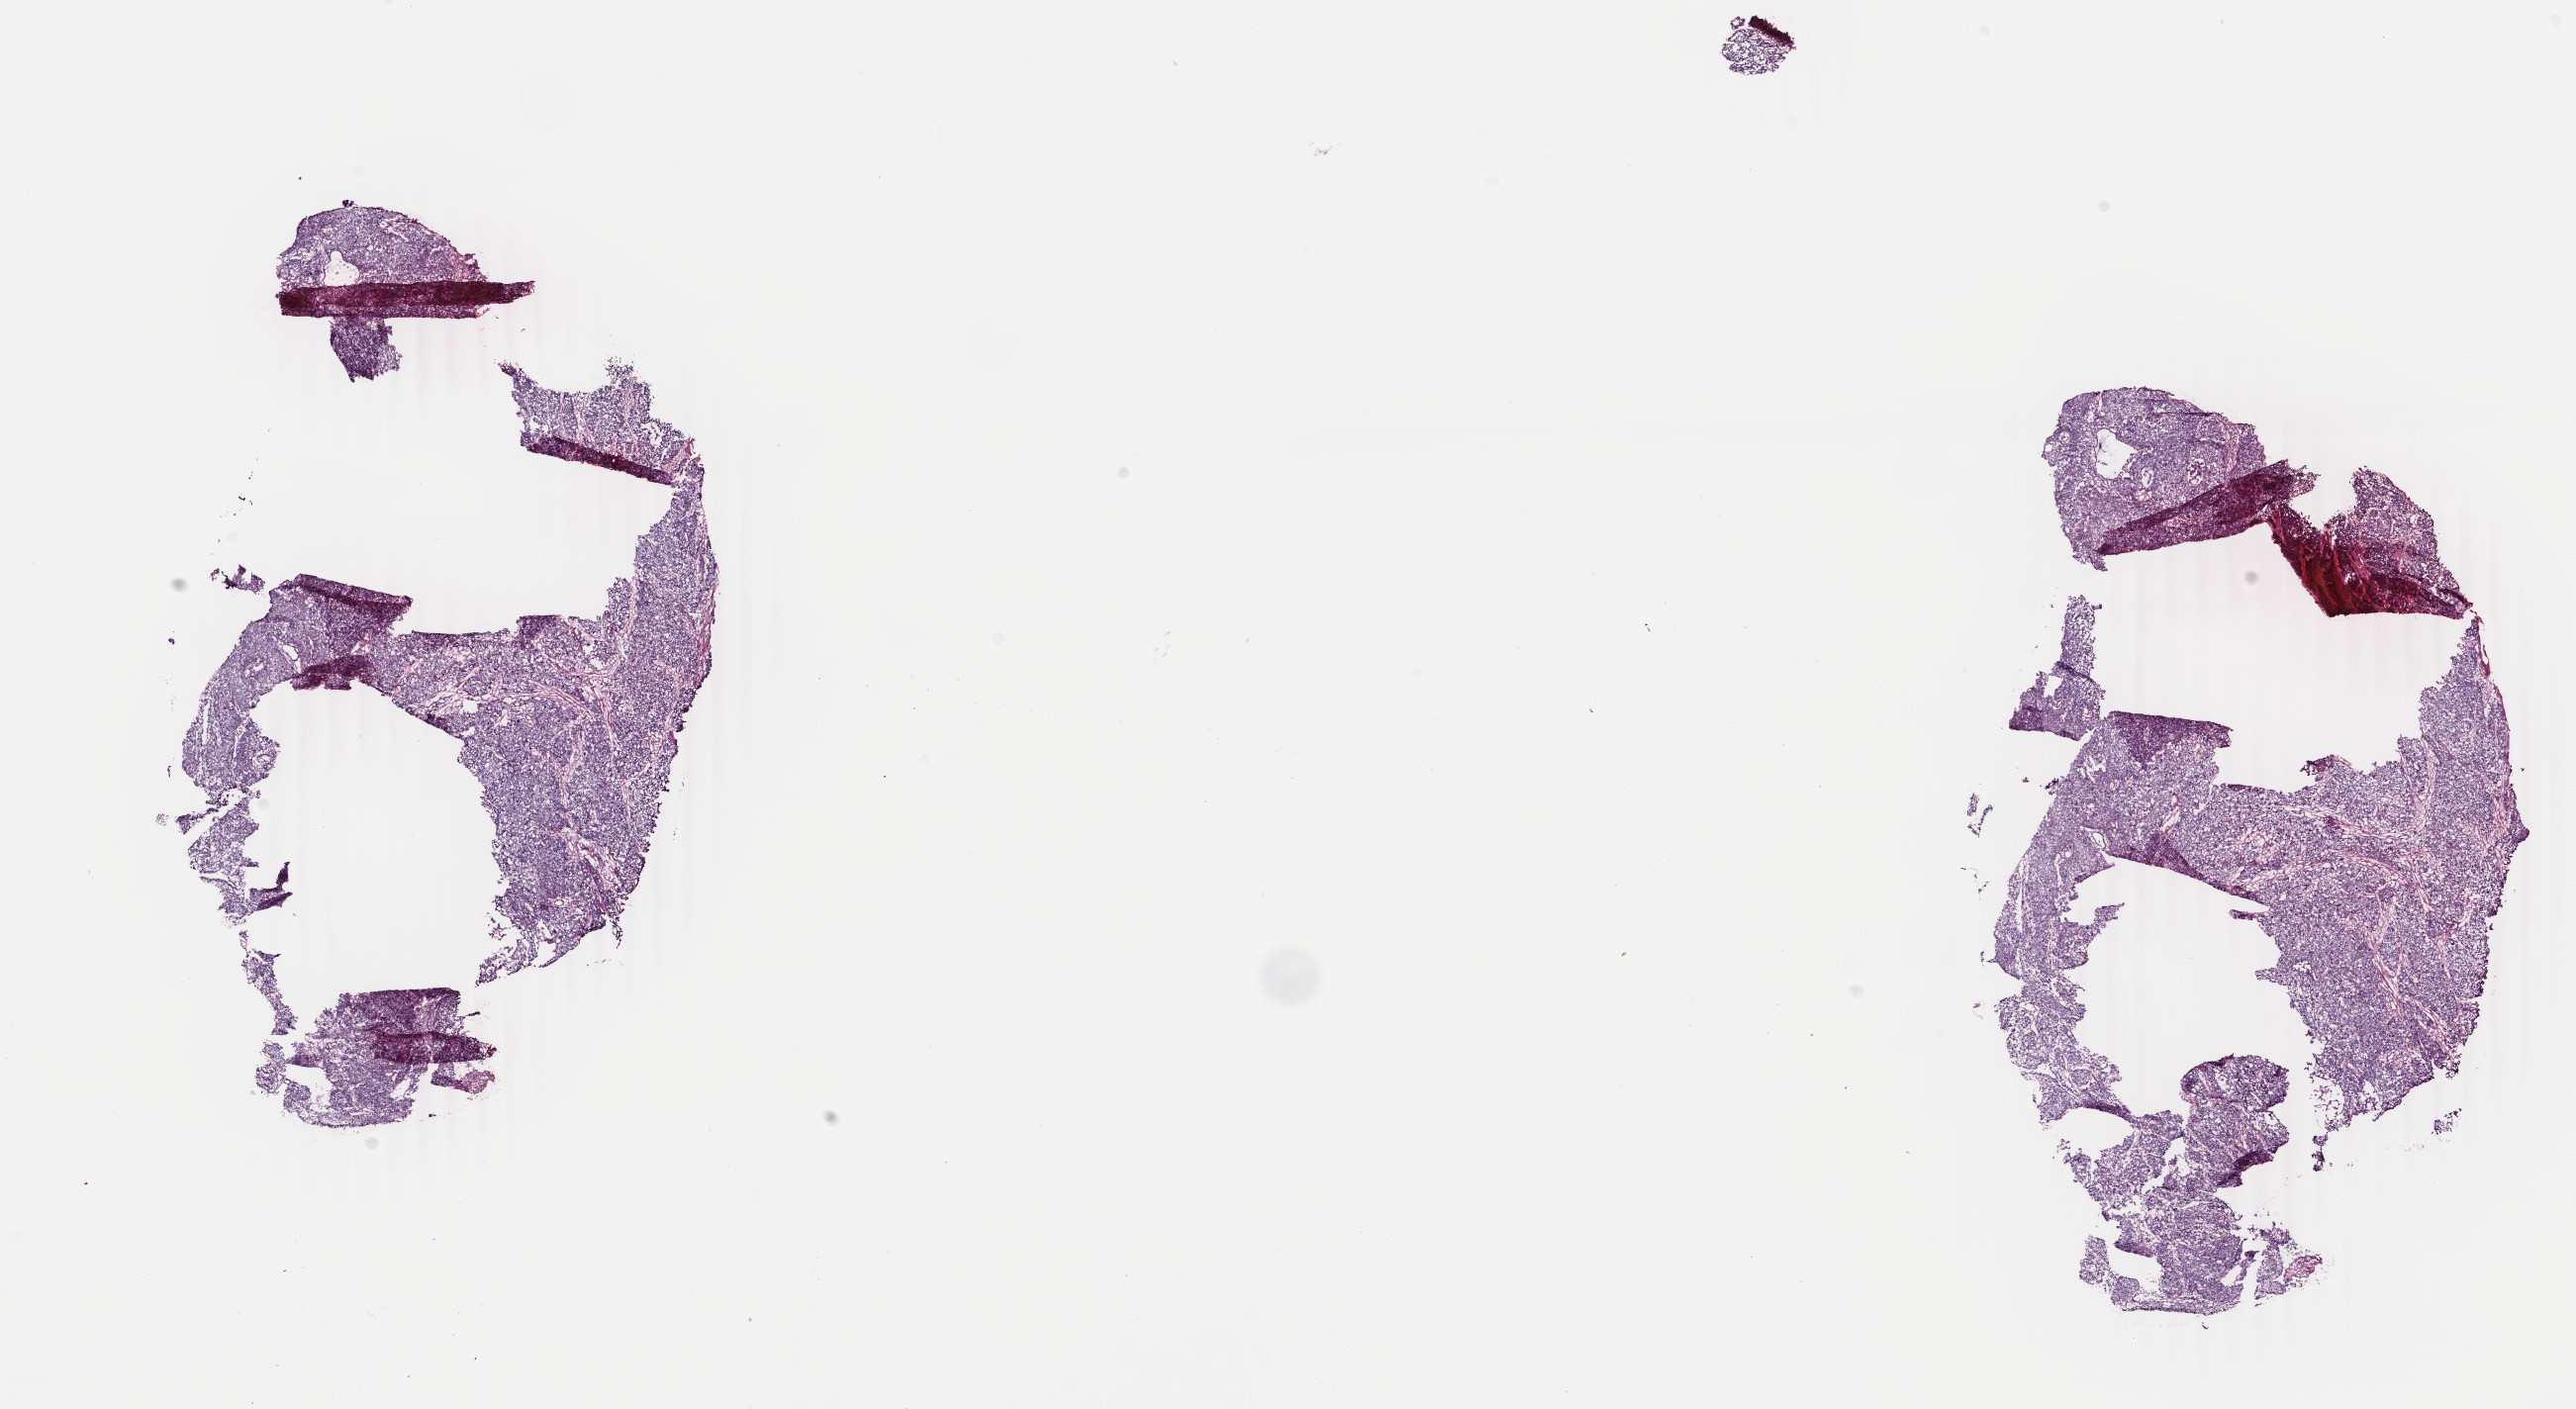
Digitized H&E tissue section (whole slide) — shown as a low-resolution overview of the whole scanned area (about 20.7 x 11.3 mm), frozen section from the top of the tissue portion, primary tumour sample from the cervix. Female, age 28 years at initial diagnosis. Histologic grade: G3 (poorly differentiated). Slide review estimates, as recorded: tumour cells 84%, tumour nuclei 85%, normal cells 0%, stromal cells 15%, necrosis 1%. Infiltration values recorded for this section: lymphocyte infiltration 2%, monocyte infiltration 0%, neutrophil infiltration 0%.
- diagnosis: Squamous cell carcinoma, large cell, nonkeratinizing, NOS (cervix uteri)
- FIGO stage: IB1